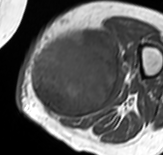
MRI of an extremity soft-tissue mass, one axial slice. Position 28 of 65 along the scan axis. MR volume resampled by the dataset authors to the PET/CT grid (not the native acquisition matrix). 163 × 155 image matrix. Female patient. Case-level facts recorded for this patient, not image findings: histological type: pleomorphic leiomyosarcoma; grade: high; site of the primary tumour: left thigh.
Outlined on this slice (expert contour drawn on MRI and transferred to this co-registered scan by the dataset authors):
- gross tumour volume including surrounding oedema: bounding box (x1, y1, x2, y2) in pixels: (30, 29, 120, 121)
- gross tumour volume (mass): (30, 29, 118, 118)